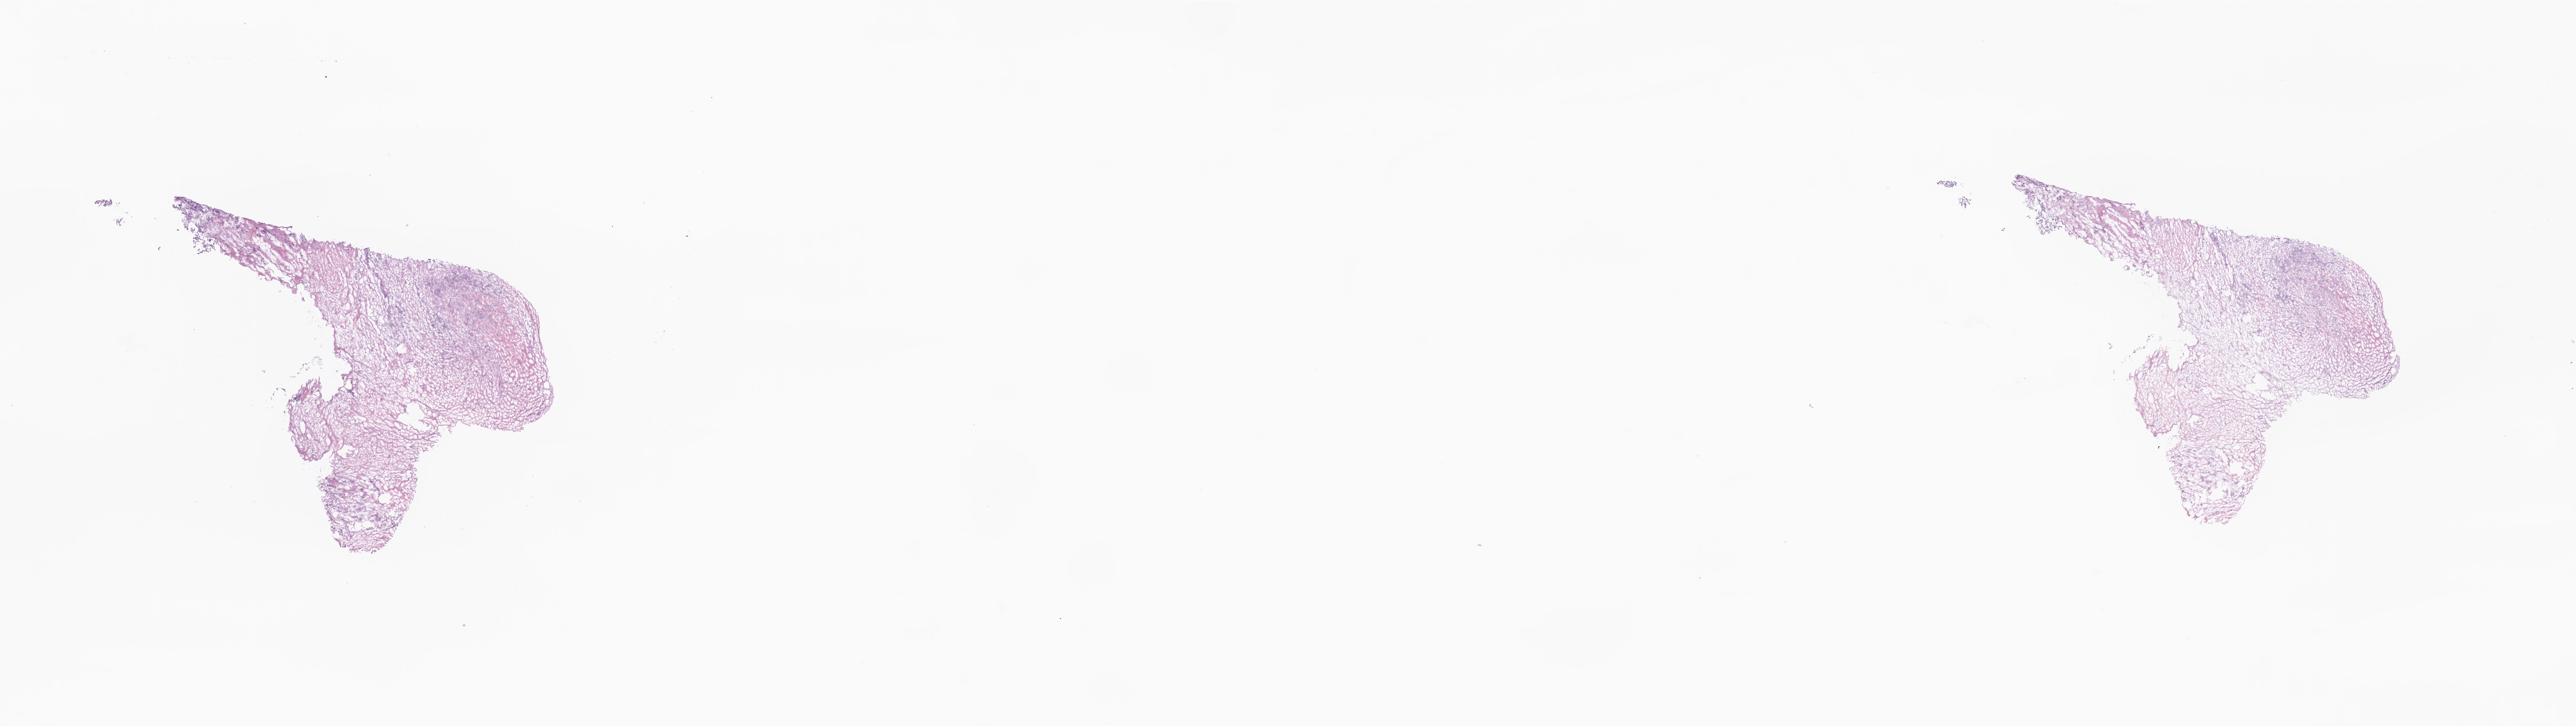
Whole-slide image, H&E stain — low-resolution overview of the scanned area, about 27.4 x 7.7 mm; frozen section; primary tumor; anatomic site: breast (right). Female patient; age at initial diagnosis 60 years. Slide review estimates, as recorded: tumor cells 5%, tumor nuclei 90%, stromal cells 95%, necrosis 0%, normal cells 0%. Inflammatory infiltration, as recorded: lymphocyte infiltration 5%, monocyte infiltration 0%, neutrophil infiltration 0%.
Section: bottom of the tissue portion. Histologic diagnosis: Infiltrating duct carcinoma, NOS.